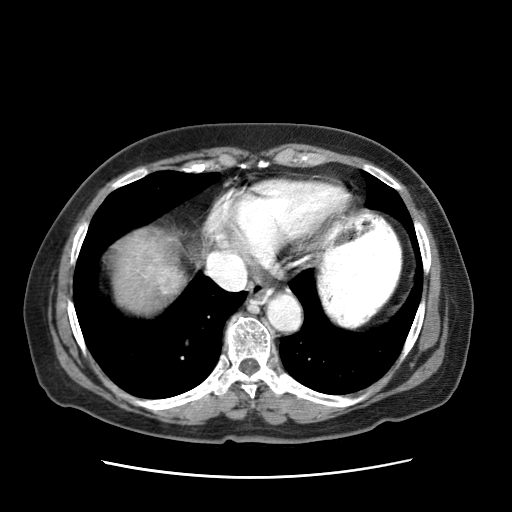
Contrast-enhanced abdominal CT (liver protocol), one axial slice. Slice 61 of 63 in the series (ordered by position). Reconstruction kernel STANDARD. 120 kVp. Intravenous contrast given. Soft-tissue window (W 400 / L 40 HU). 2.5 mm slice thickness. 512 × 512 image matrix, field of view 360 × 360 mm. Female patient, age 79 years. Case-level facts recorded for this patient, not image findings: diagnosis: hepatocellular carcinoma (patient treated with transarterial chemoembolisation; whether this scan precedes or follows treatment is not stated here); TNM stage (as recorded): Stage-II; Child-Pugh class: B.
Annotated regions visible in this slice (semi-automatic segmentation, software-assisted and operator-edited):
- abdominal aorta: box from (x=265, y=293) to (x=300, y=330) px
- liver parenchyma outside the tumour (the mass and vessels are separate outlines, so this box may not span the whole liver): (x=102, y=227)–(x=185, y=317)
- mass: (x=157, y=264)–(x=190, y=295)
- liver vessels: (x=137, y=251)–(x=247, y=290)